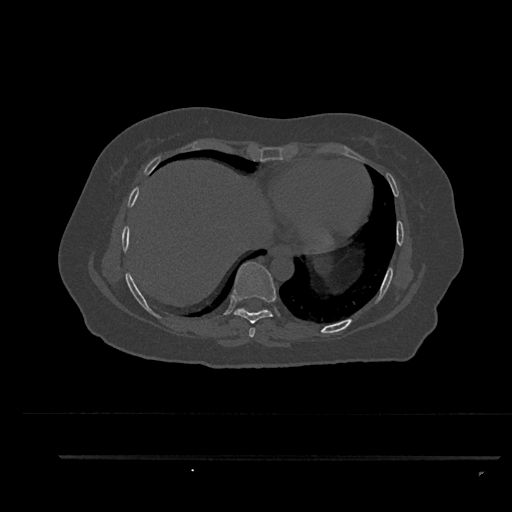
CT including the spine, one axial slice; slice 453 of 797 in the series (ordered by position); reconstruction kernel Br40s/3; bone window (W 1800 / L 400 HU); 0.5 mm slice thickness; 512 × 512 image matrix, field of view 408 × 408 mm. Patient: female, 44 years. Case-level facts recorded for this patient, not image findings: primary cancer: renal; vertebrae with lytic lesions (as recorded): L1.
Outlined on this slice (semi-automatically segmented with operator editing):
- T7 vertebra: box from (x=249, y=328) to (x=256, y=338) px
- T8 vertebra: (x=233, y=262)–(x=276, y=324)
- T9 vertebra: (x=234, y=308)–(x=267, y=313)